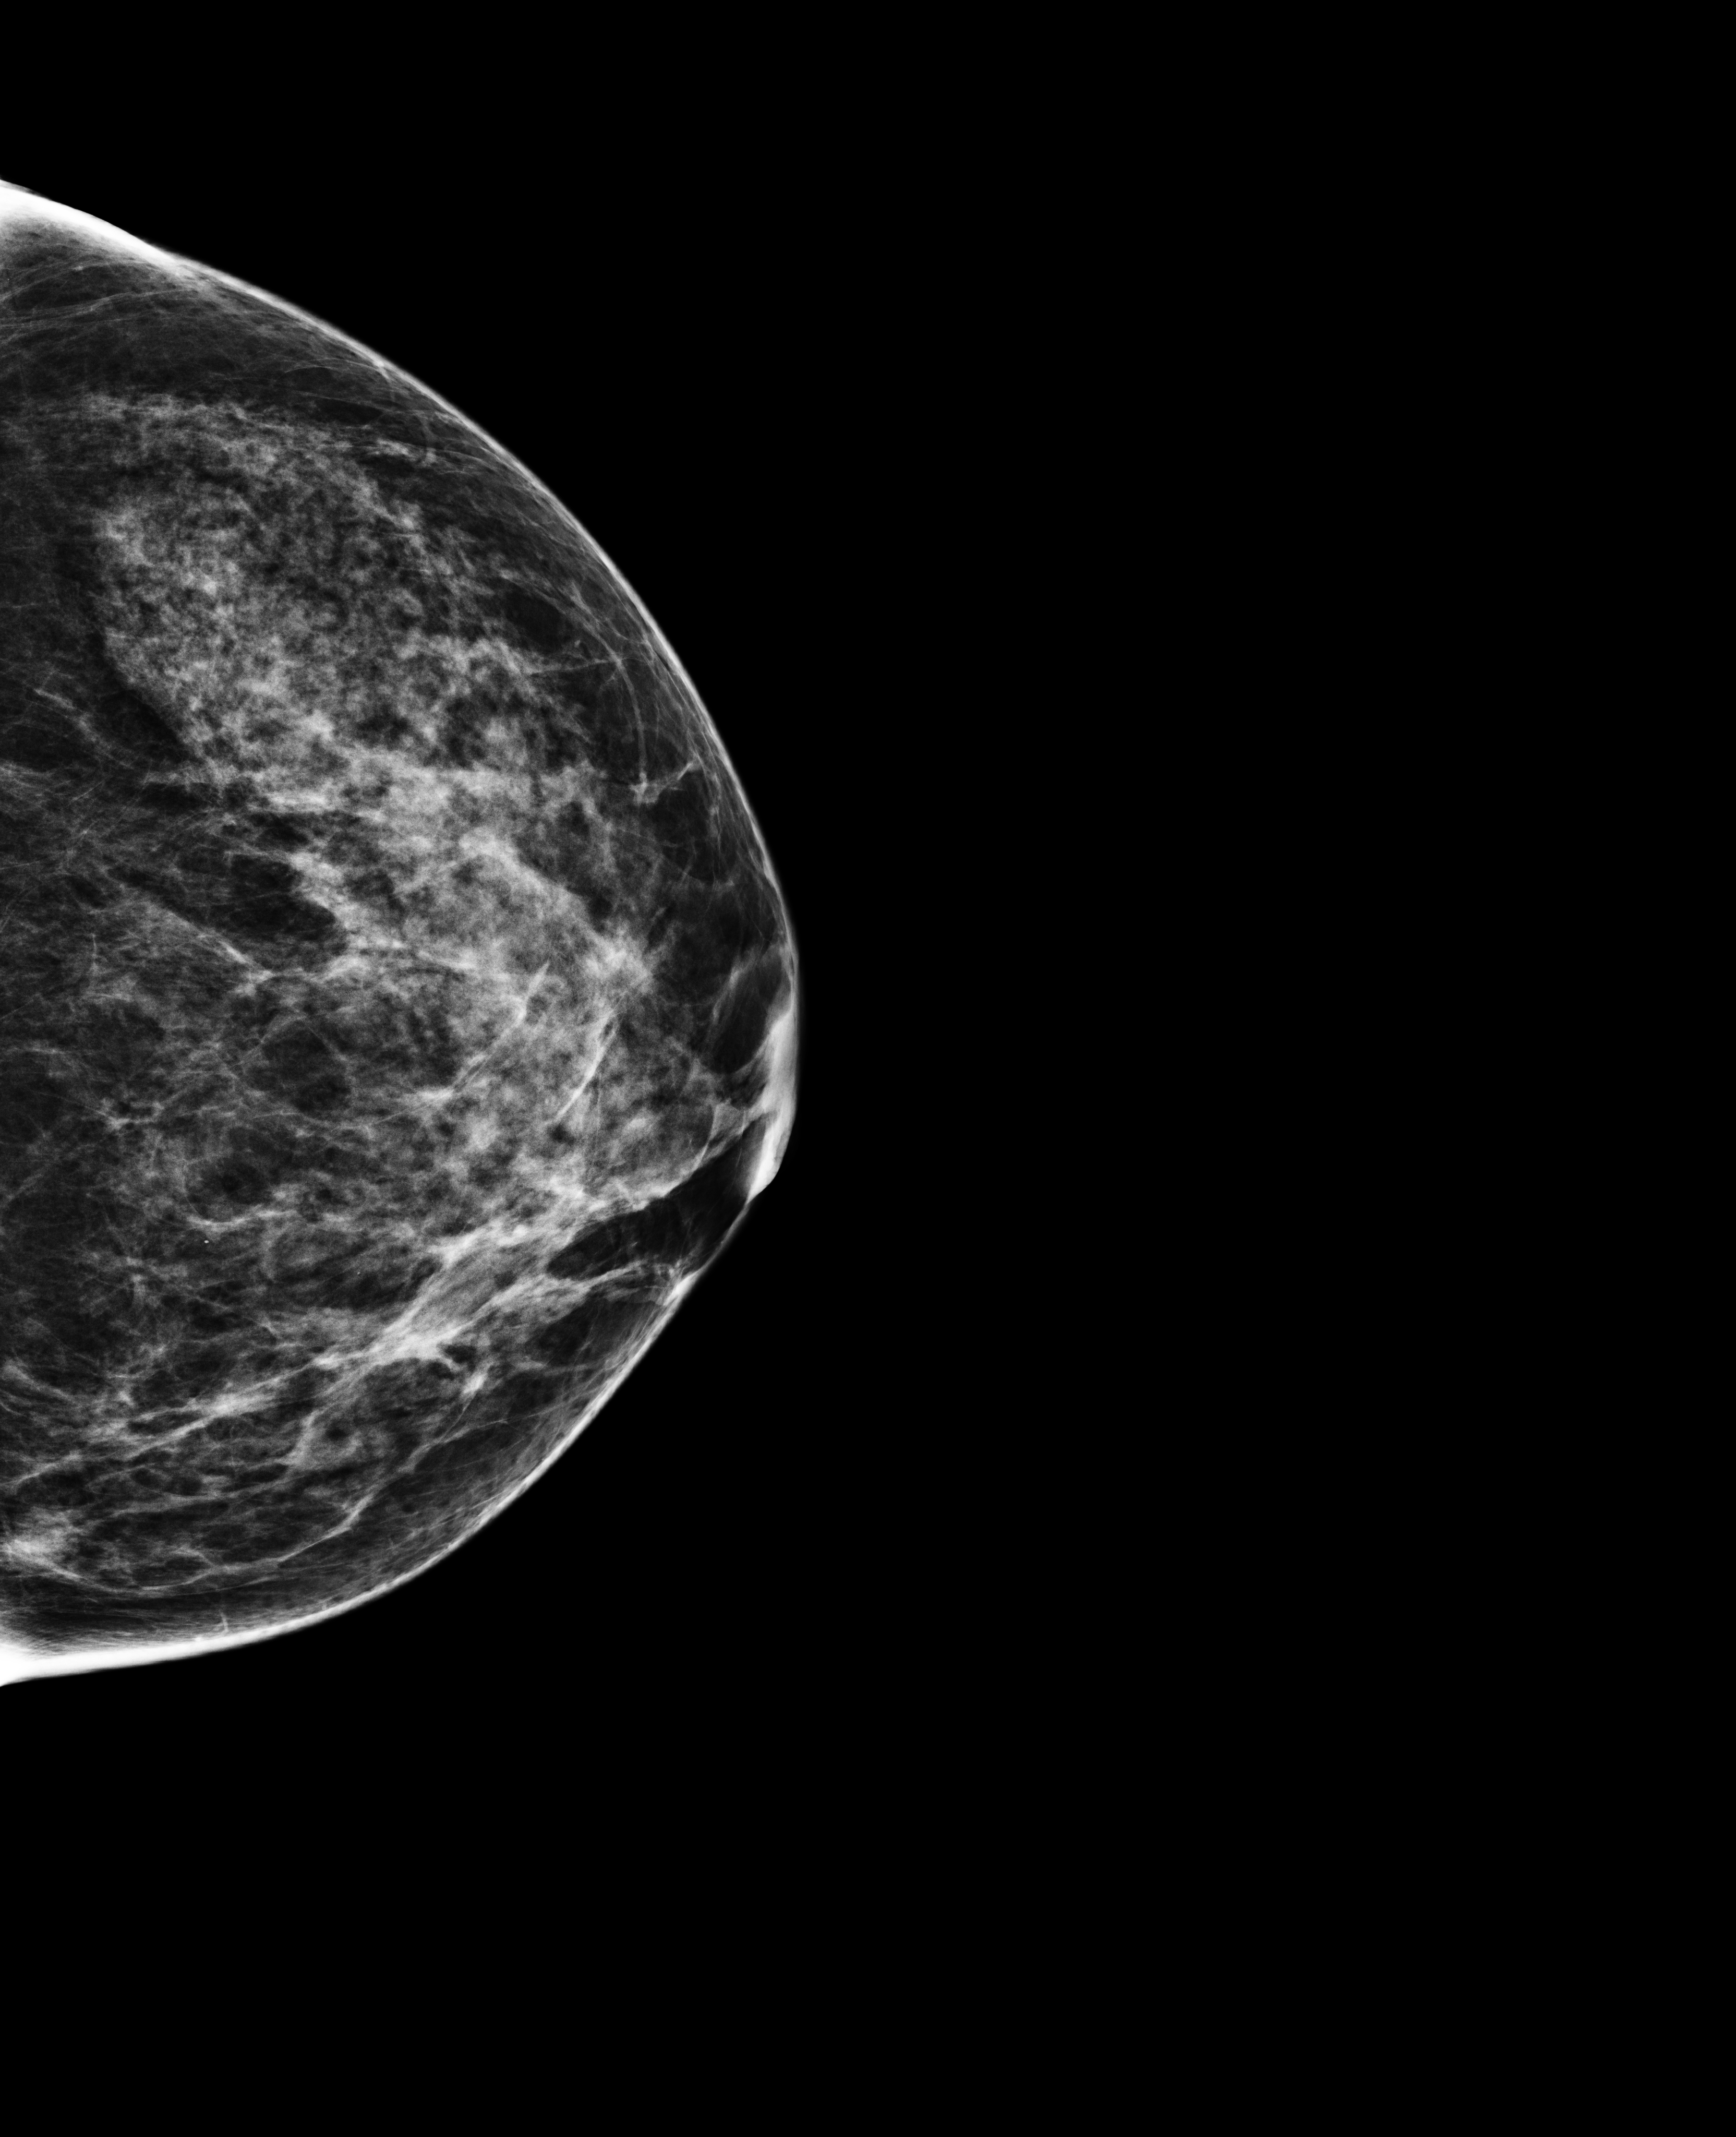
Annual screening mammography examination, compressed breast thickness 57 mm, system: Selenia Dimensions. Patient: female, 47 years.
Image type: full-field digital mammogram. Breast: left. Projection: craniocaudal (CC) view.